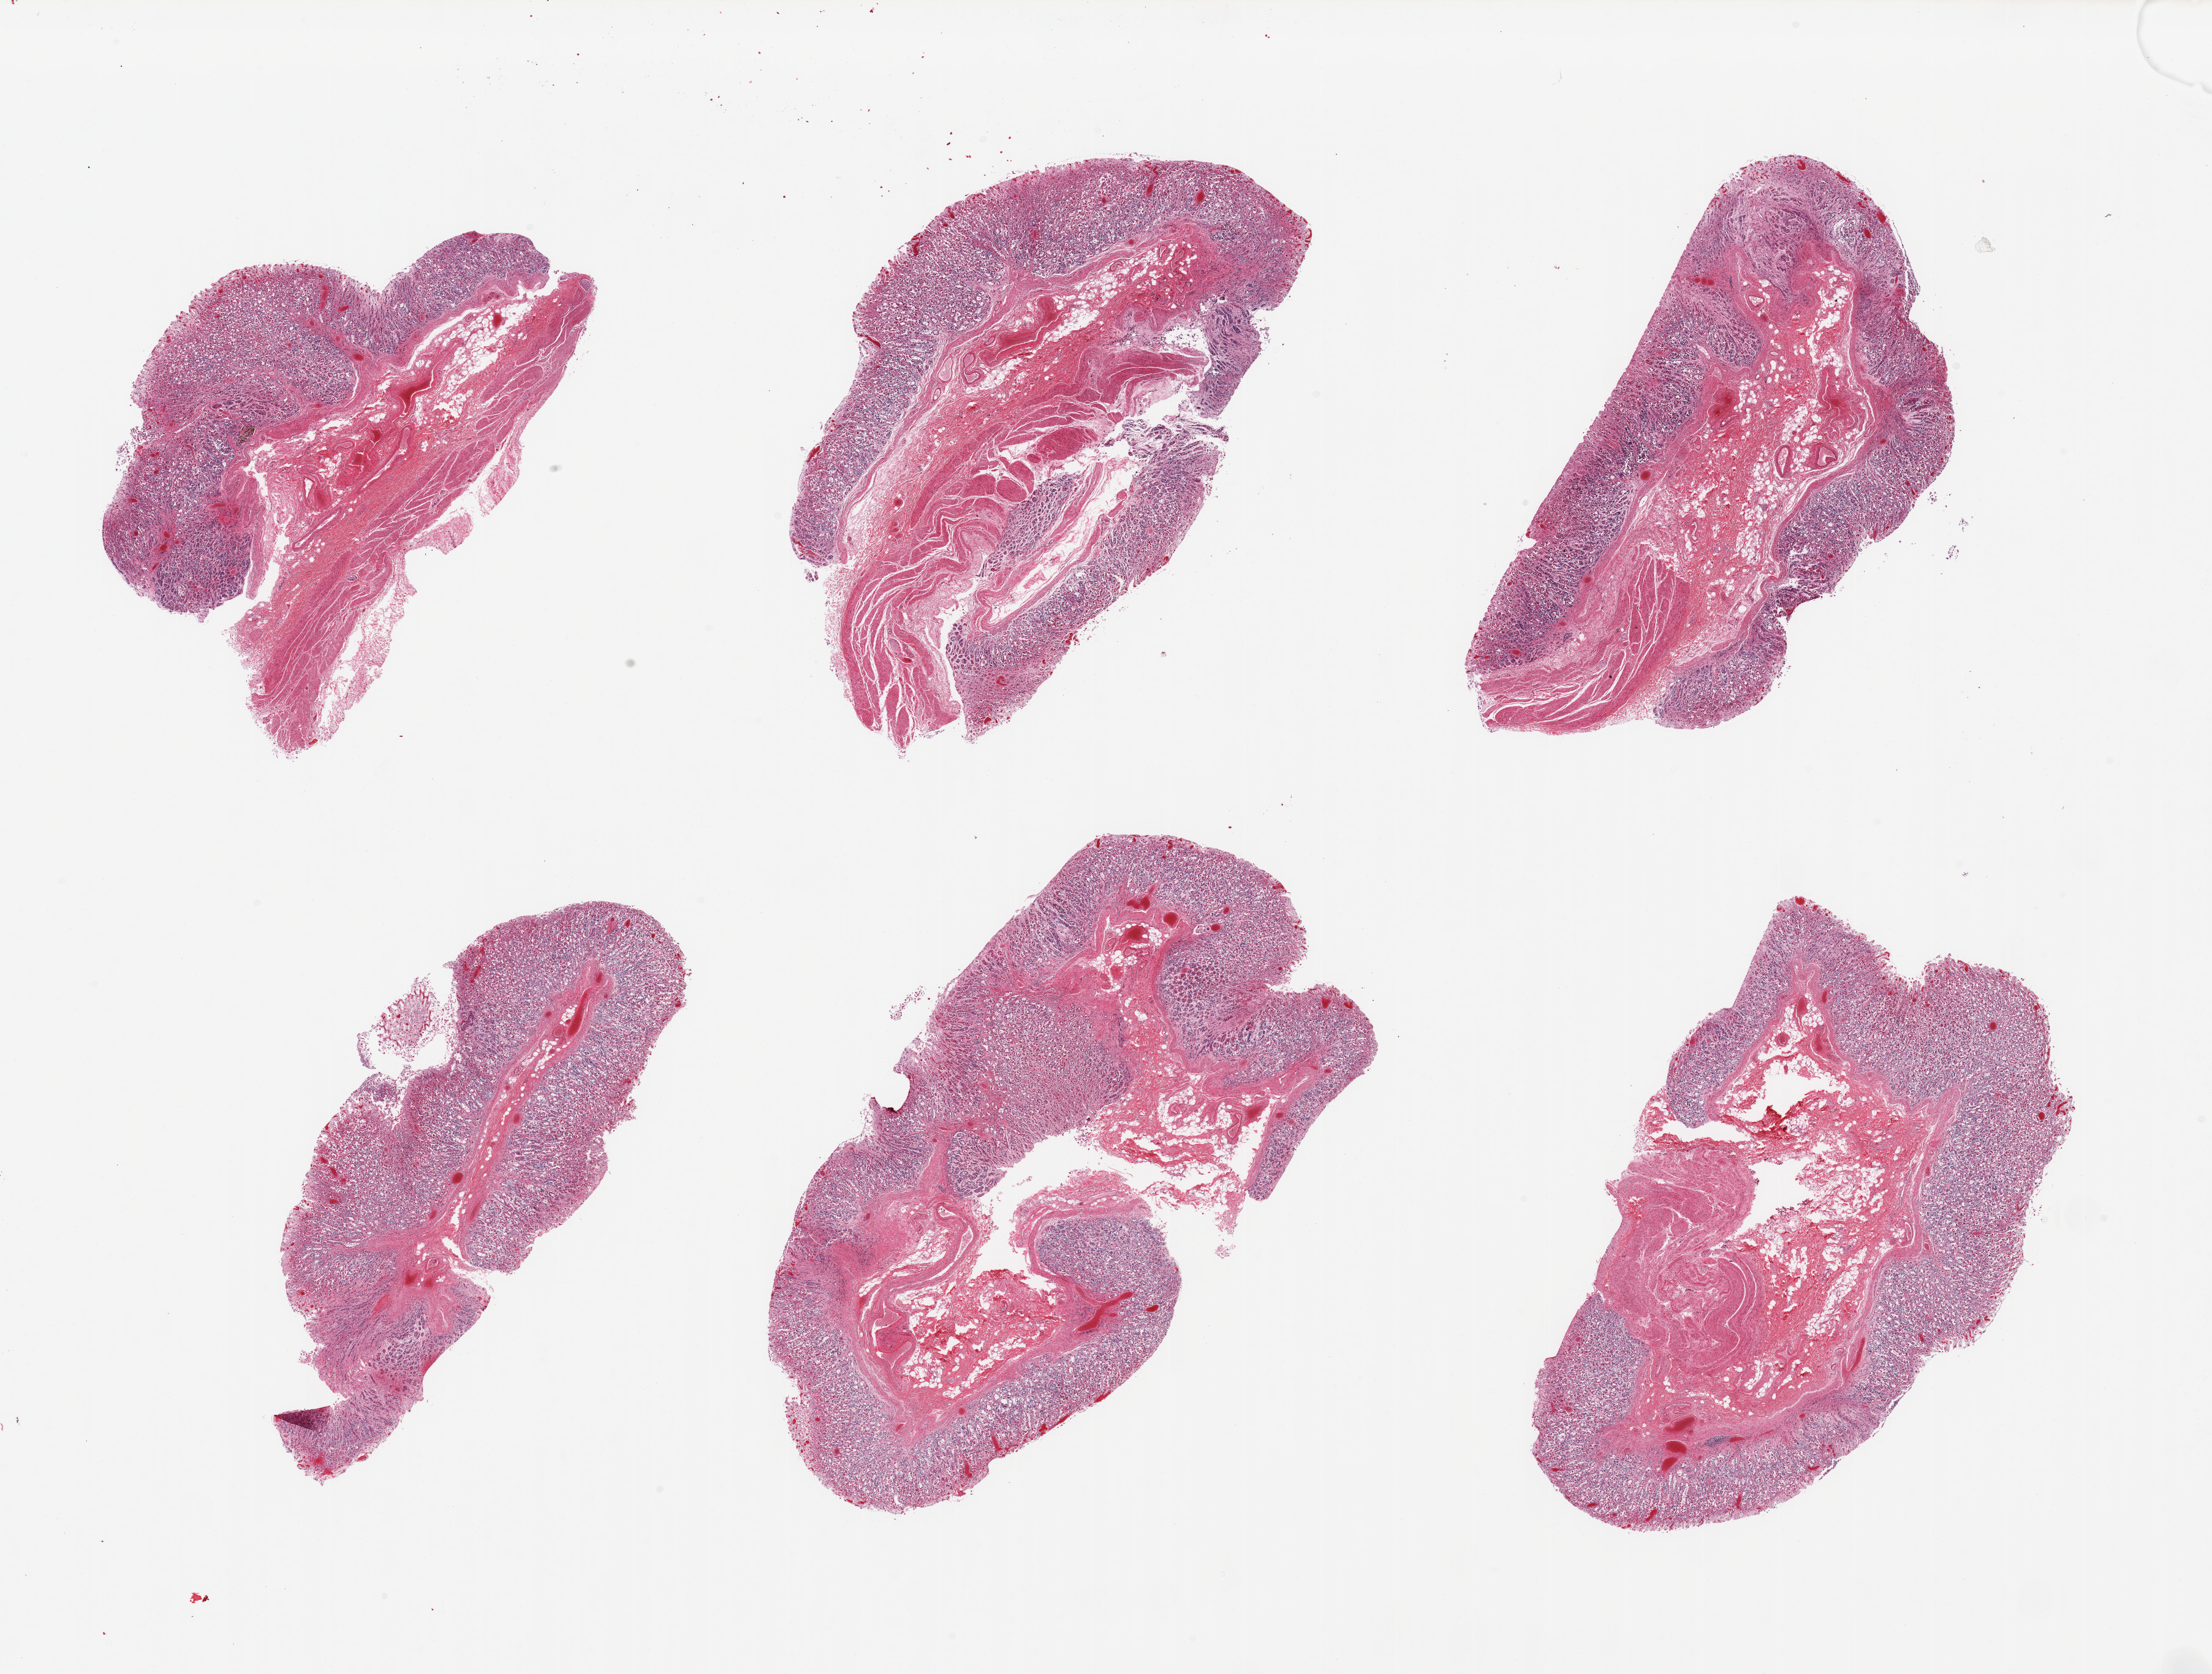
Digitized hematoxylin and eosin (H&E)-stained section, low-resolution overview of the scanned area, about 28.5 x 21.6 mm (from a 20x scan). PAXgene-fixed paraffin-embedded (PFPE) section. Target tissue: stomach. Donor tissue sample. Donor: male.
Reviewer comment on this tissue sample: 6 pieces, mucosa up to ~1mm, ~80-90% thickness, moderately advanced autolysis.